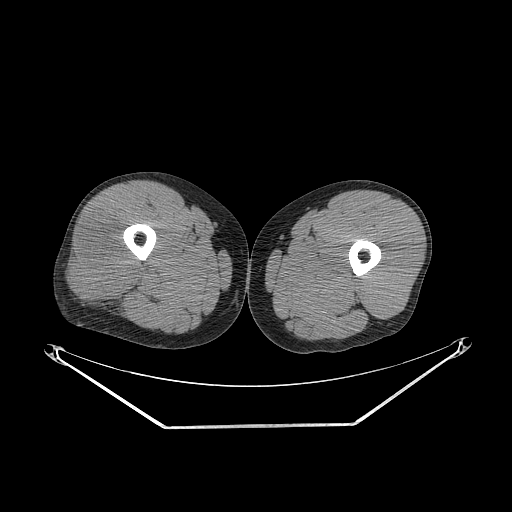
CT of an extremity soft-tissue mass (from a PET/CT study), one axial slice; position 243 of 267 along the scan axis; reconstruction kernel STANDARD; 140 kVp; soft-tissue window (W 400 / L 40 HU); 3.75 mm slice thickness; 512 × 512 image matrix, field of view 500 × 500 mm. Male patient. Case-level facts recorded for this patient, not image findings: histological type: poorly differentiated synovial sarcoma; grade: high; site of the primary tumour: right buttock.
Annotated regions visible in this slice (expert contour drawn on MRI and transferred to this co-registered scan by the dataset authors):
- gross tumour volume including surrounding oedema: bounding box <73,223,136,305> (left, top, right, bottom; pixels)
- gross tumour volume (mass): <73,224,136,305>